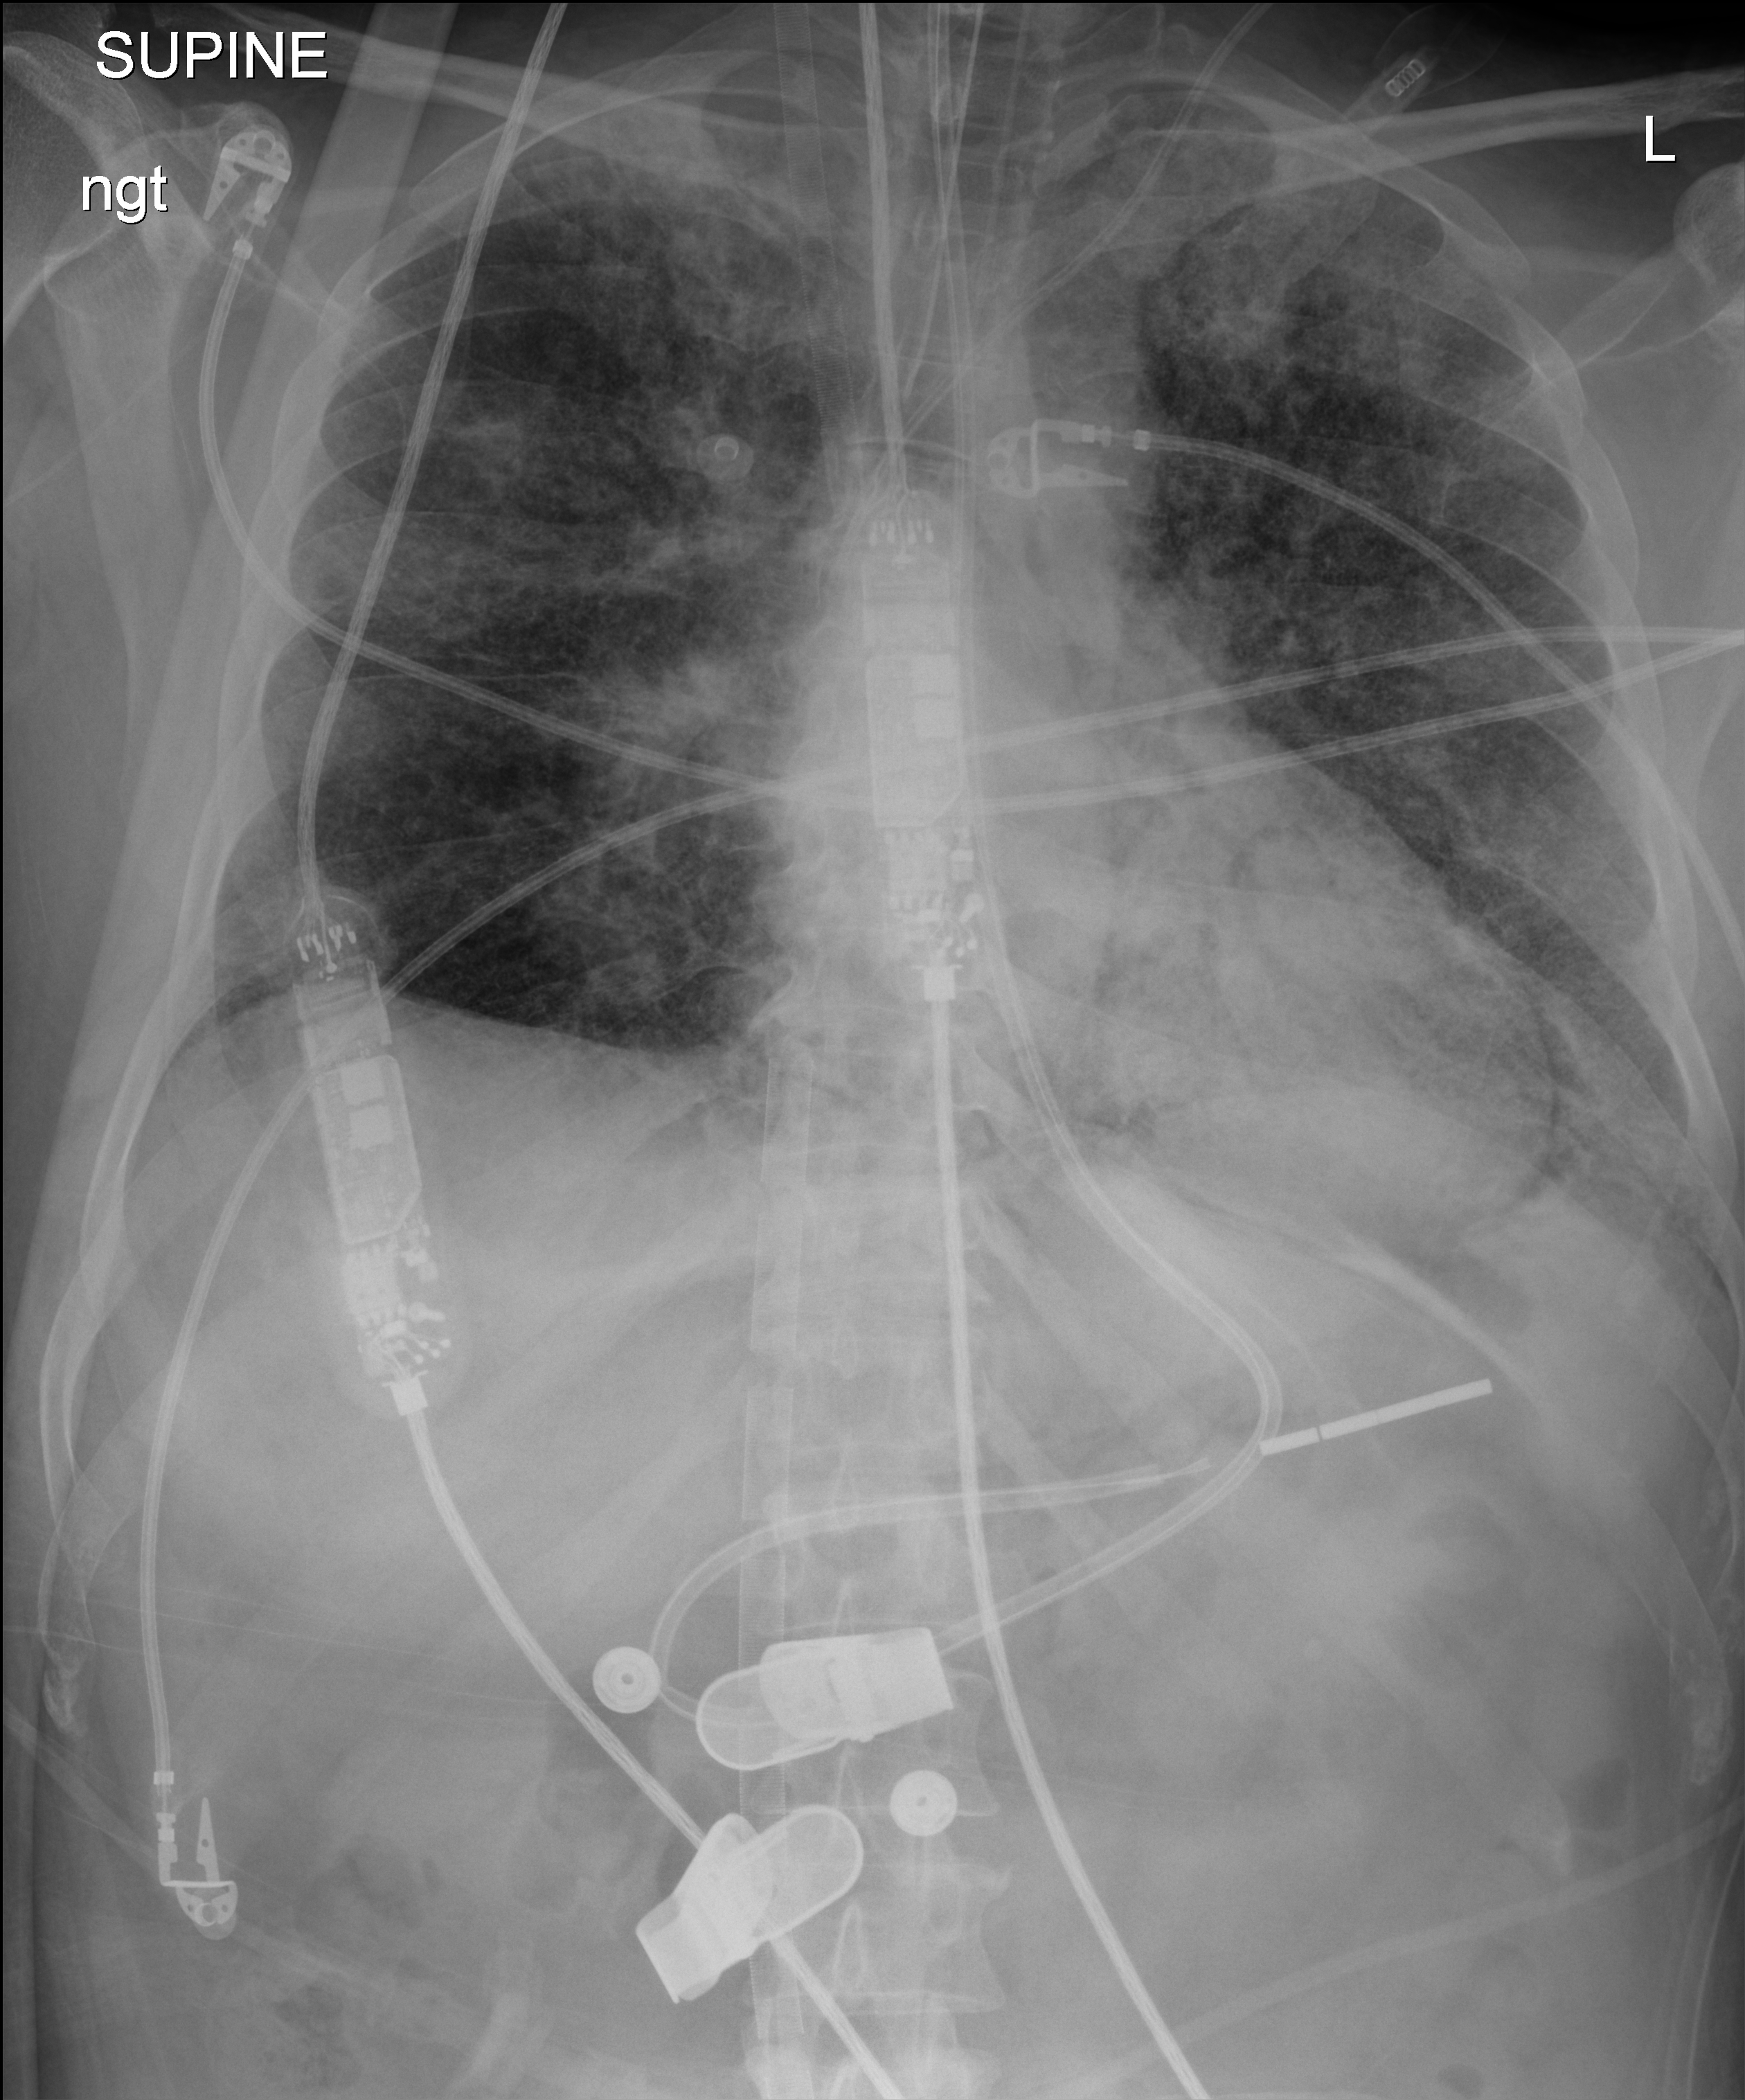
Bedside chest radiograph (digital radiography), anteroposterior (AP) projection. Male patient hospitalised with COVID-19, age 18–59 years.
Hospital-stay facts (about this admission, not read from this image; timing relative to this image not recorded):
- admitted to intensive care during this hospital stay: yes
- length of hospital stay: 42 days
- mechanically ventilated during this hospital stay: yes